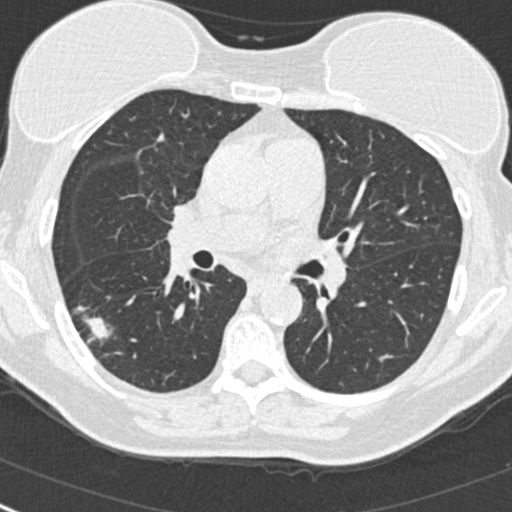
Low-dose screening chest CT, one axial slice. Slice 150 of 268 in the series (ordered by position). Reconstruction kernel B30f. 120 kVp. Lung window (W 1500 / L -600 HU). 1 mm slice thickness. 512 × 512 image matrix, field of view 296 × 296 mm.
Structures marked on this image (outlined manually by an expert reader):
- lesion 1 (tumor, upper lobe of right lung): bounding box <74,306,111,340> (left, top, right, bottom; pixels)